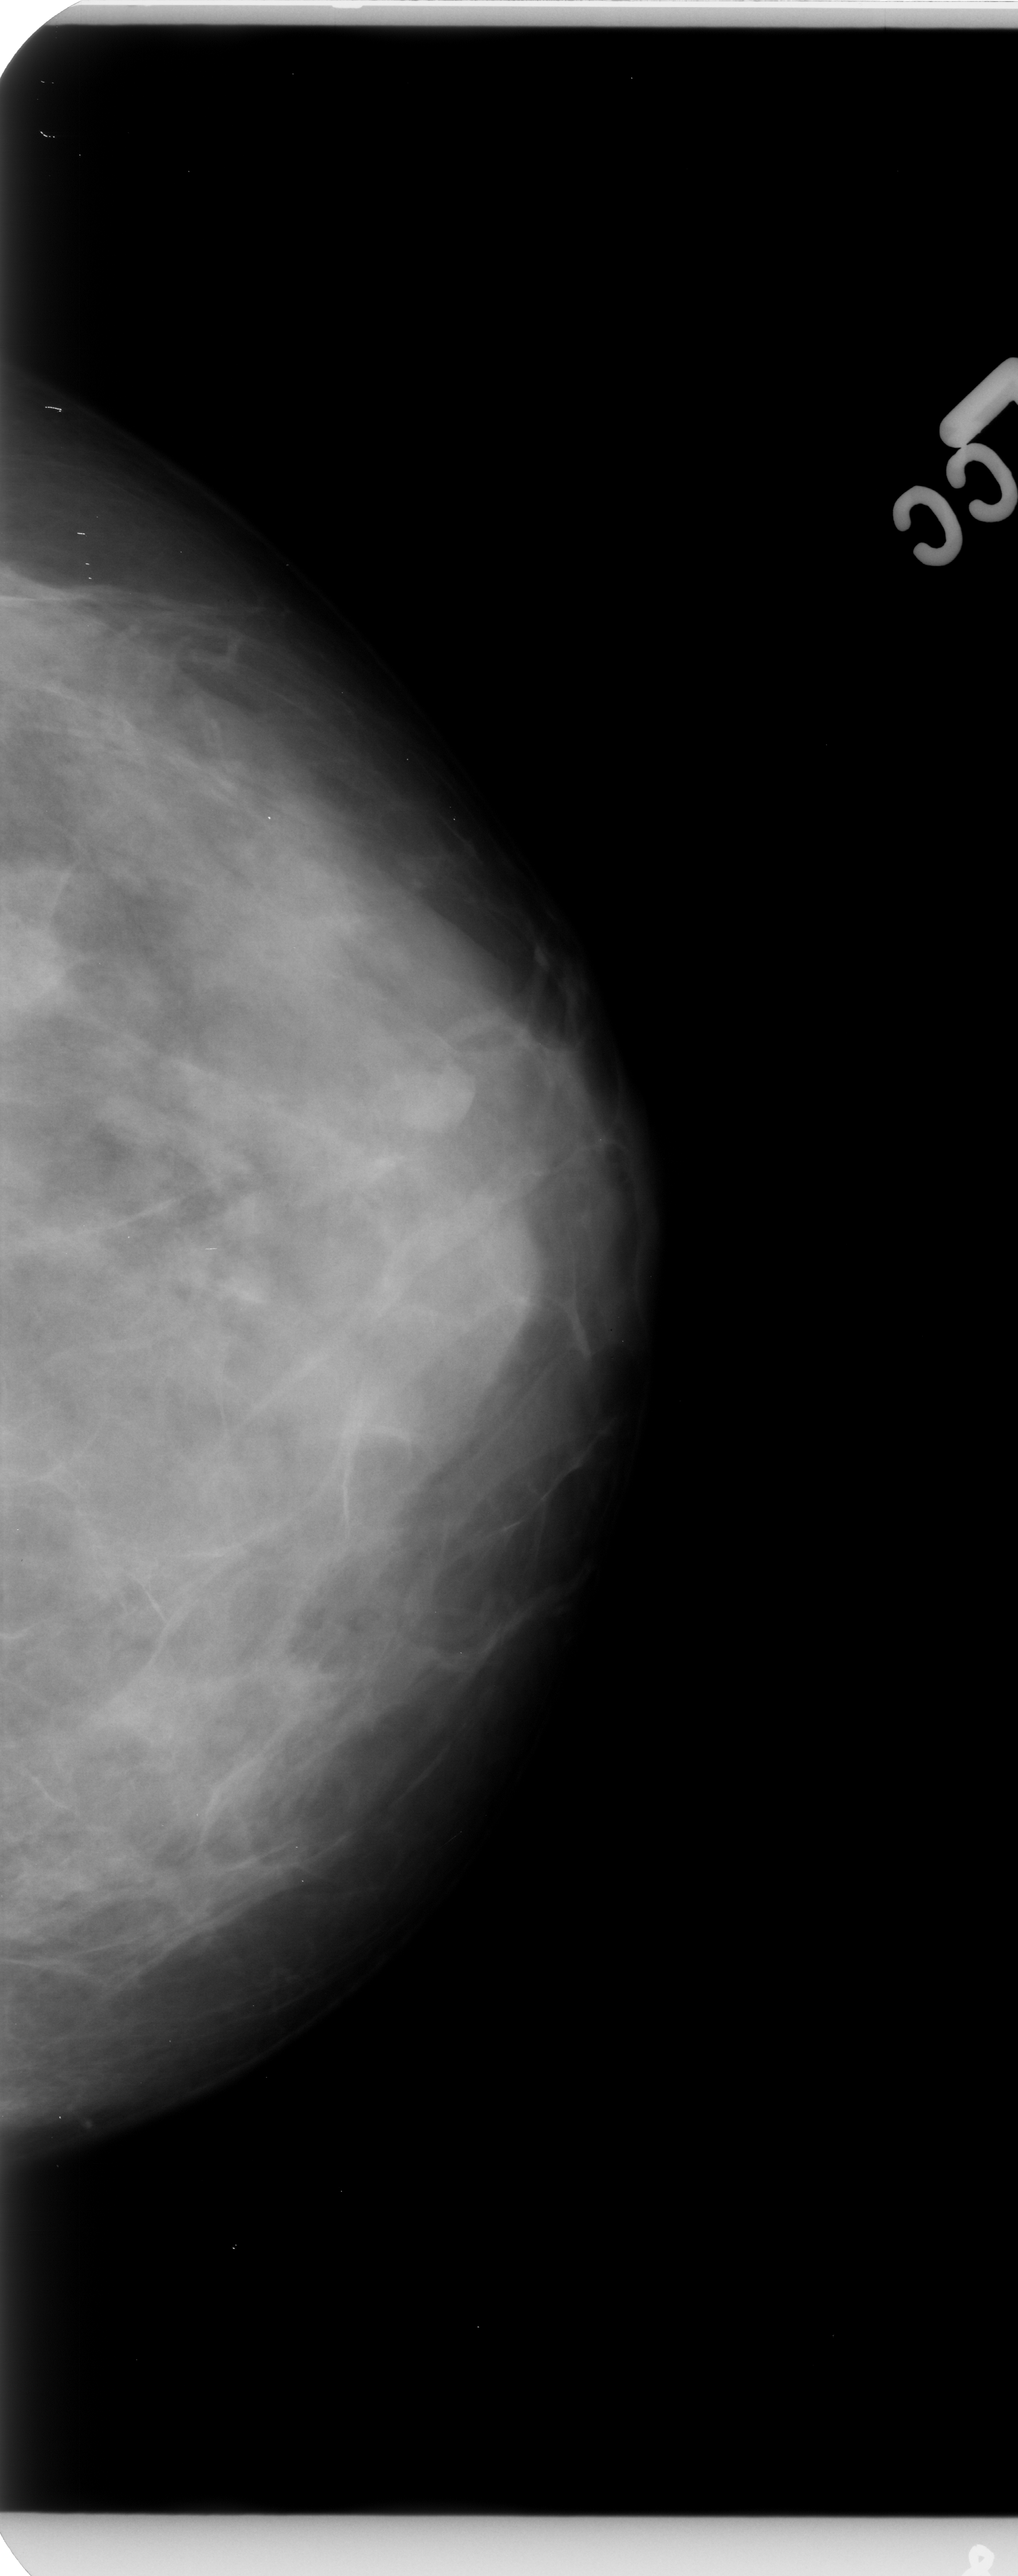
Digitized screen-film mammogram. Left breast. CC view. BI-RADS breast density category 4 (scale 1–4). 1018 × 2576 image matrix.
Expert-marked regions of interest on this film, with their recorded descriptors:
- mass, shape irregular, margins circumscribed / obscured; BI-RADS assessment category 4; subtlety rating 3 on a 1 (subtle) to 5 (obvious) scale; pathology (as recorded): benign: bounding box [x1, y1, x2, y2] px = [382, 1053, 480, 1132]